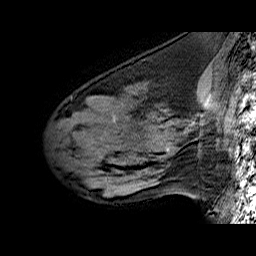
Breast MRI (dynamic contrast-enhanced), one sagittal slice. Dynamic contrast-enhanced series, time point 2 of 6 at this slice position (early post-contrast). 1.5 T. TE 6.4 ms, TR 32.9 ms. 4 mm slice thickness. 256 × 256 image matrix. Female patient. Case-level facts recorded for this patient, not image findings: setting: breast cancer imaged before/during neoadjuvant chemotherapy; receptor status: HER2-positive.
Outlined on this slice (semi-automatic segmentation, software-assisted and operator-edited):
- analysis volume of interest (the breast-tissue region the enhancement analysis was run in; not a lesion): bounding box [x1, y1, x2, y2] px = [55, 81, 196, 160]
- tumour enhancement mask (voxels above the 100 % enhancement threshold inside the analysis volume of interest): [167, 148, 169, 151]